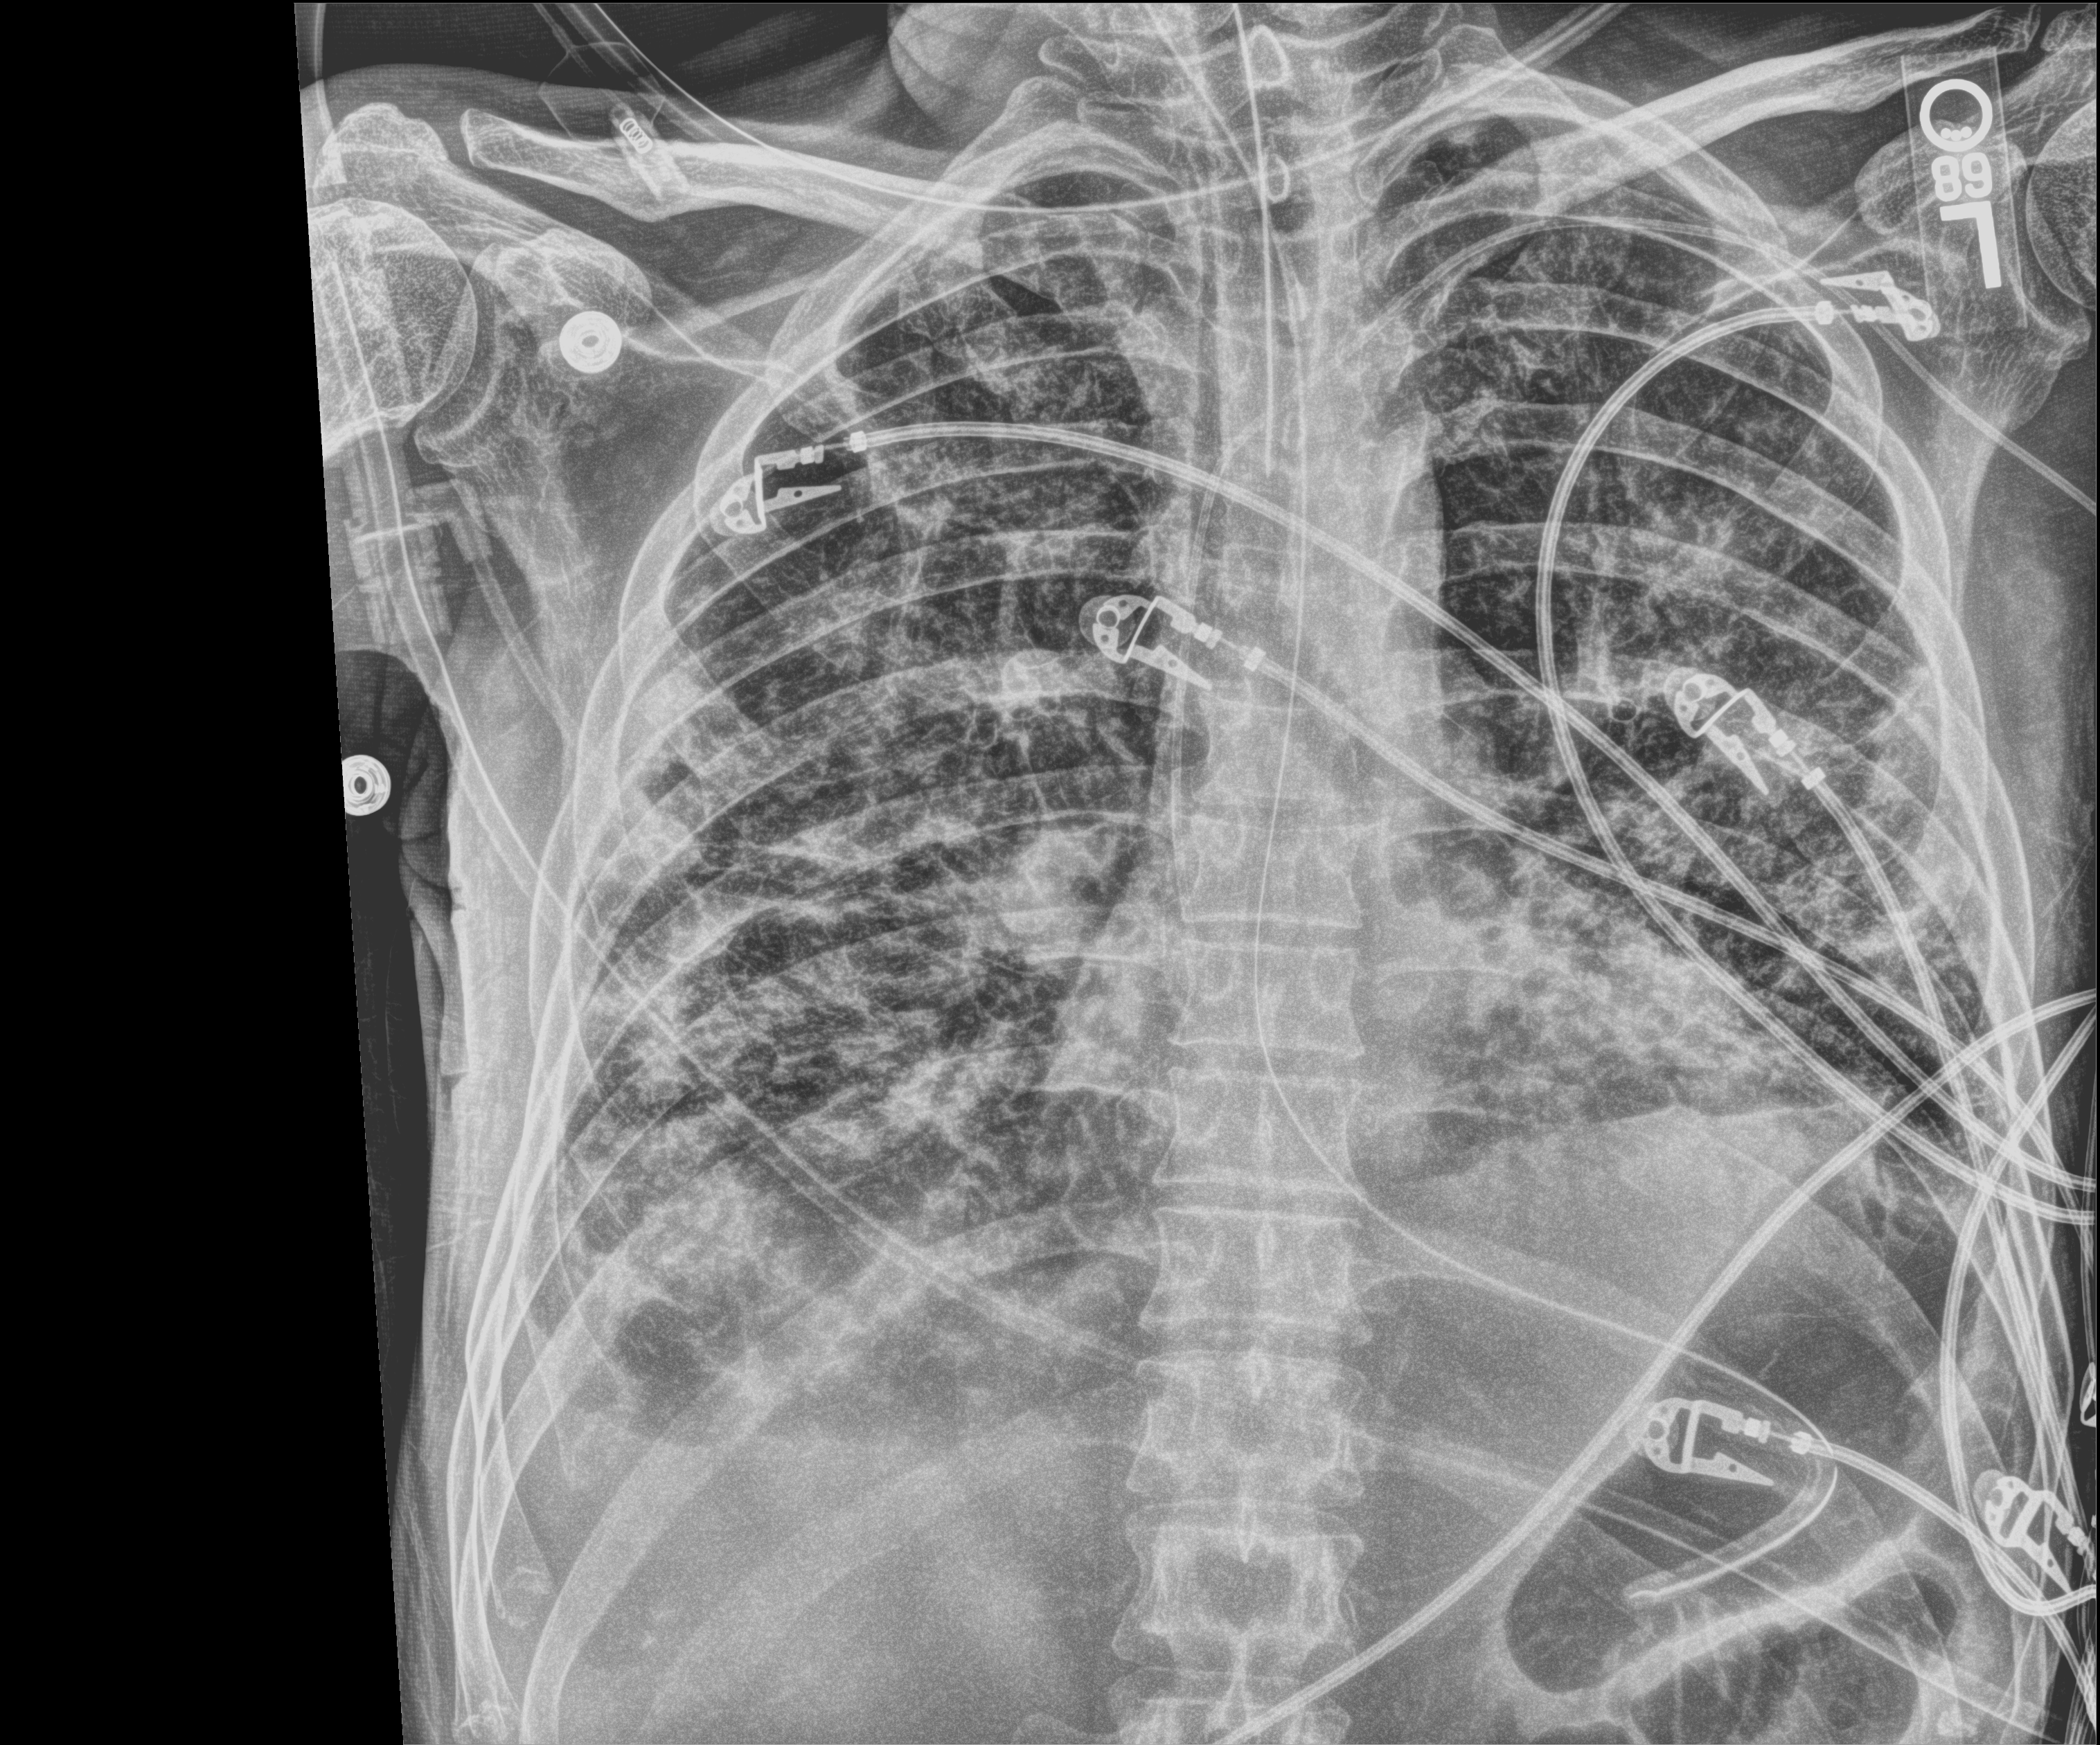
Chest radiograph (digital radiography). Male patient hospitalised with COVID-19, age 18–59 years.
Hospital-stay facts (about this admission, not read from this image; timing relative to this image not recorded): length of hospital stay: 96 days.